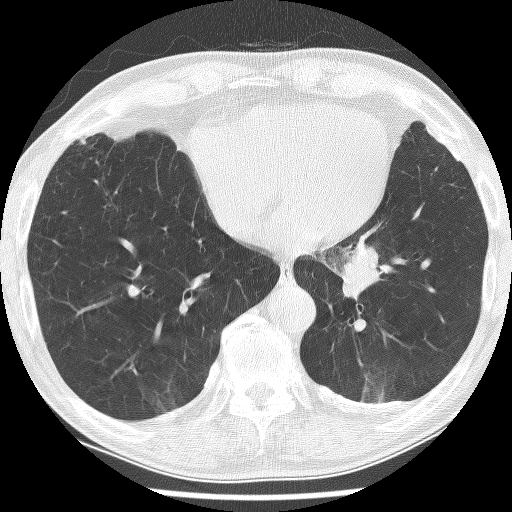
Axial slice from a low-dose chest CT screening exam; baseline annual screen; lung window (W 1500 / L -600 HU); 2.5 mm slice thickness; lung (sharp) reconstruction kernel (BONE); 120 kVp; slice 170 of 226 in the series; 512 × 512 image matrix, field of view 320 × 320 mm. Male, age 74 years at enrolment. Current smoker at enrolment.
- Lesion marked by an expert reader, bounding box <317,228,424,321> (left, top, right, bottom; pixels).
- Reader record for this screening exam (exam-level; its link to the box is not recorded): non-calcified nodule or mass ≥4 mm, left lower lobe, 30 × 27 mm, spiculated (stellate) margins, soft tissue attenuation.
- Official screen result: positive, change unspecified: nodule(s) >= 4 mm or enlarging nodule(s), mass(es), or other non-specific abnormalities suspicious for lung cancer.
- Later outcome: lung cancer diagnosed 151 days after this screen — adenocarcinoma, NOS, left lower lobe, stage IIIA (AJCC 6th edition), 49 mm at pathology.